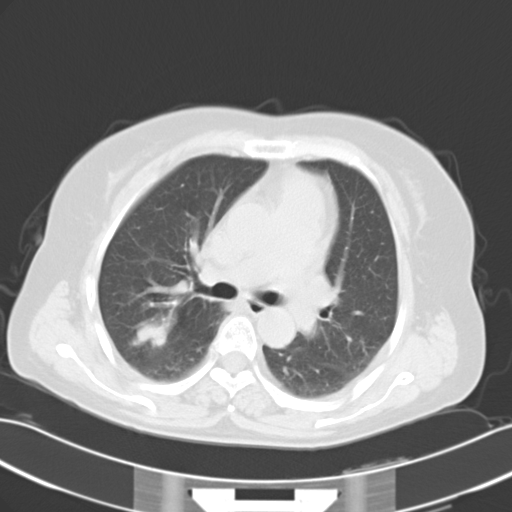
Chest CT, one axial slice. Slice 22 of 35 in the series (ordered by position). Reconstruction kernel B40f. 120 kVp. Lung window (W 1500 / L -600 HU). 512 × 512 image matrix, field of view 353 × 353 mm. Patient: female, 52 years. Case-level facts recorded for this patient, not image findings: clinical TNM (as recorded): T1c N3 M1a.
Structures marked on this image (rectangle marked by the reading radiologist):
- lung tumour (recorded histology: adenocarcinoma): bounding box [x1, y1, x2, y2] px = [126, 306, 187, 355]